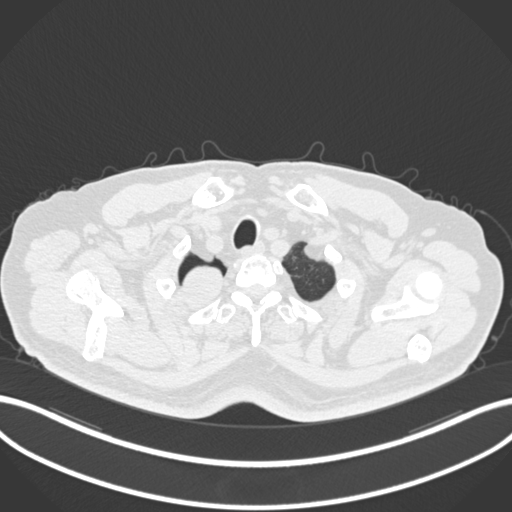
Chest CT, one axial slice; slice 200 of 218 in the series (ordered by position); 120 kVp; lung window (W 1500 / L -600 HU); 1 mm slice thickness; 512 × 512 image matrix, field of view 400 × 400 mm. Patient: male, 68 years. Case-level facts recorded for this patient, not image findings: clinical TNM (as recorded): T2a N0 M0.
Structures marked on this image (bounding box drawn by a radiologist):
- lung tumour (recorded histology: adenocarcinoma): bounding box (x1, y1, x2, y2) in pixels: (179, 262, 232, 305)